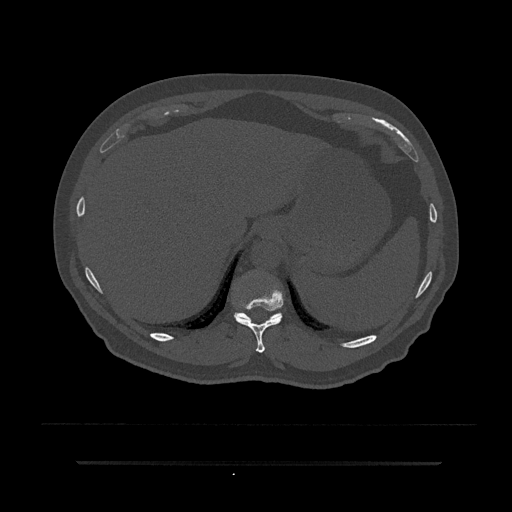
CT including the spine, one axial slice. Position 307 of 797 along the scan axis. Reconstruction kernel Br40s/3. 120 kVp. Bone window (W 1800 / L 400 HU). 512 × 512 image matrix, field of view 464 × 464 mm. Male patient, age 59 years. Case-level facts recorded for this patient, not image findings: primary cancer: bile ducts.
Structures marked on this image (semi-automatic segmentation, software-assisted and operator-edited):
- T10 vertebra: bounding box (x1, y1, x2, y2) in pixels: (234, 284, 284, 353)
- T11 vertebra: (234, 312, 282, 322)